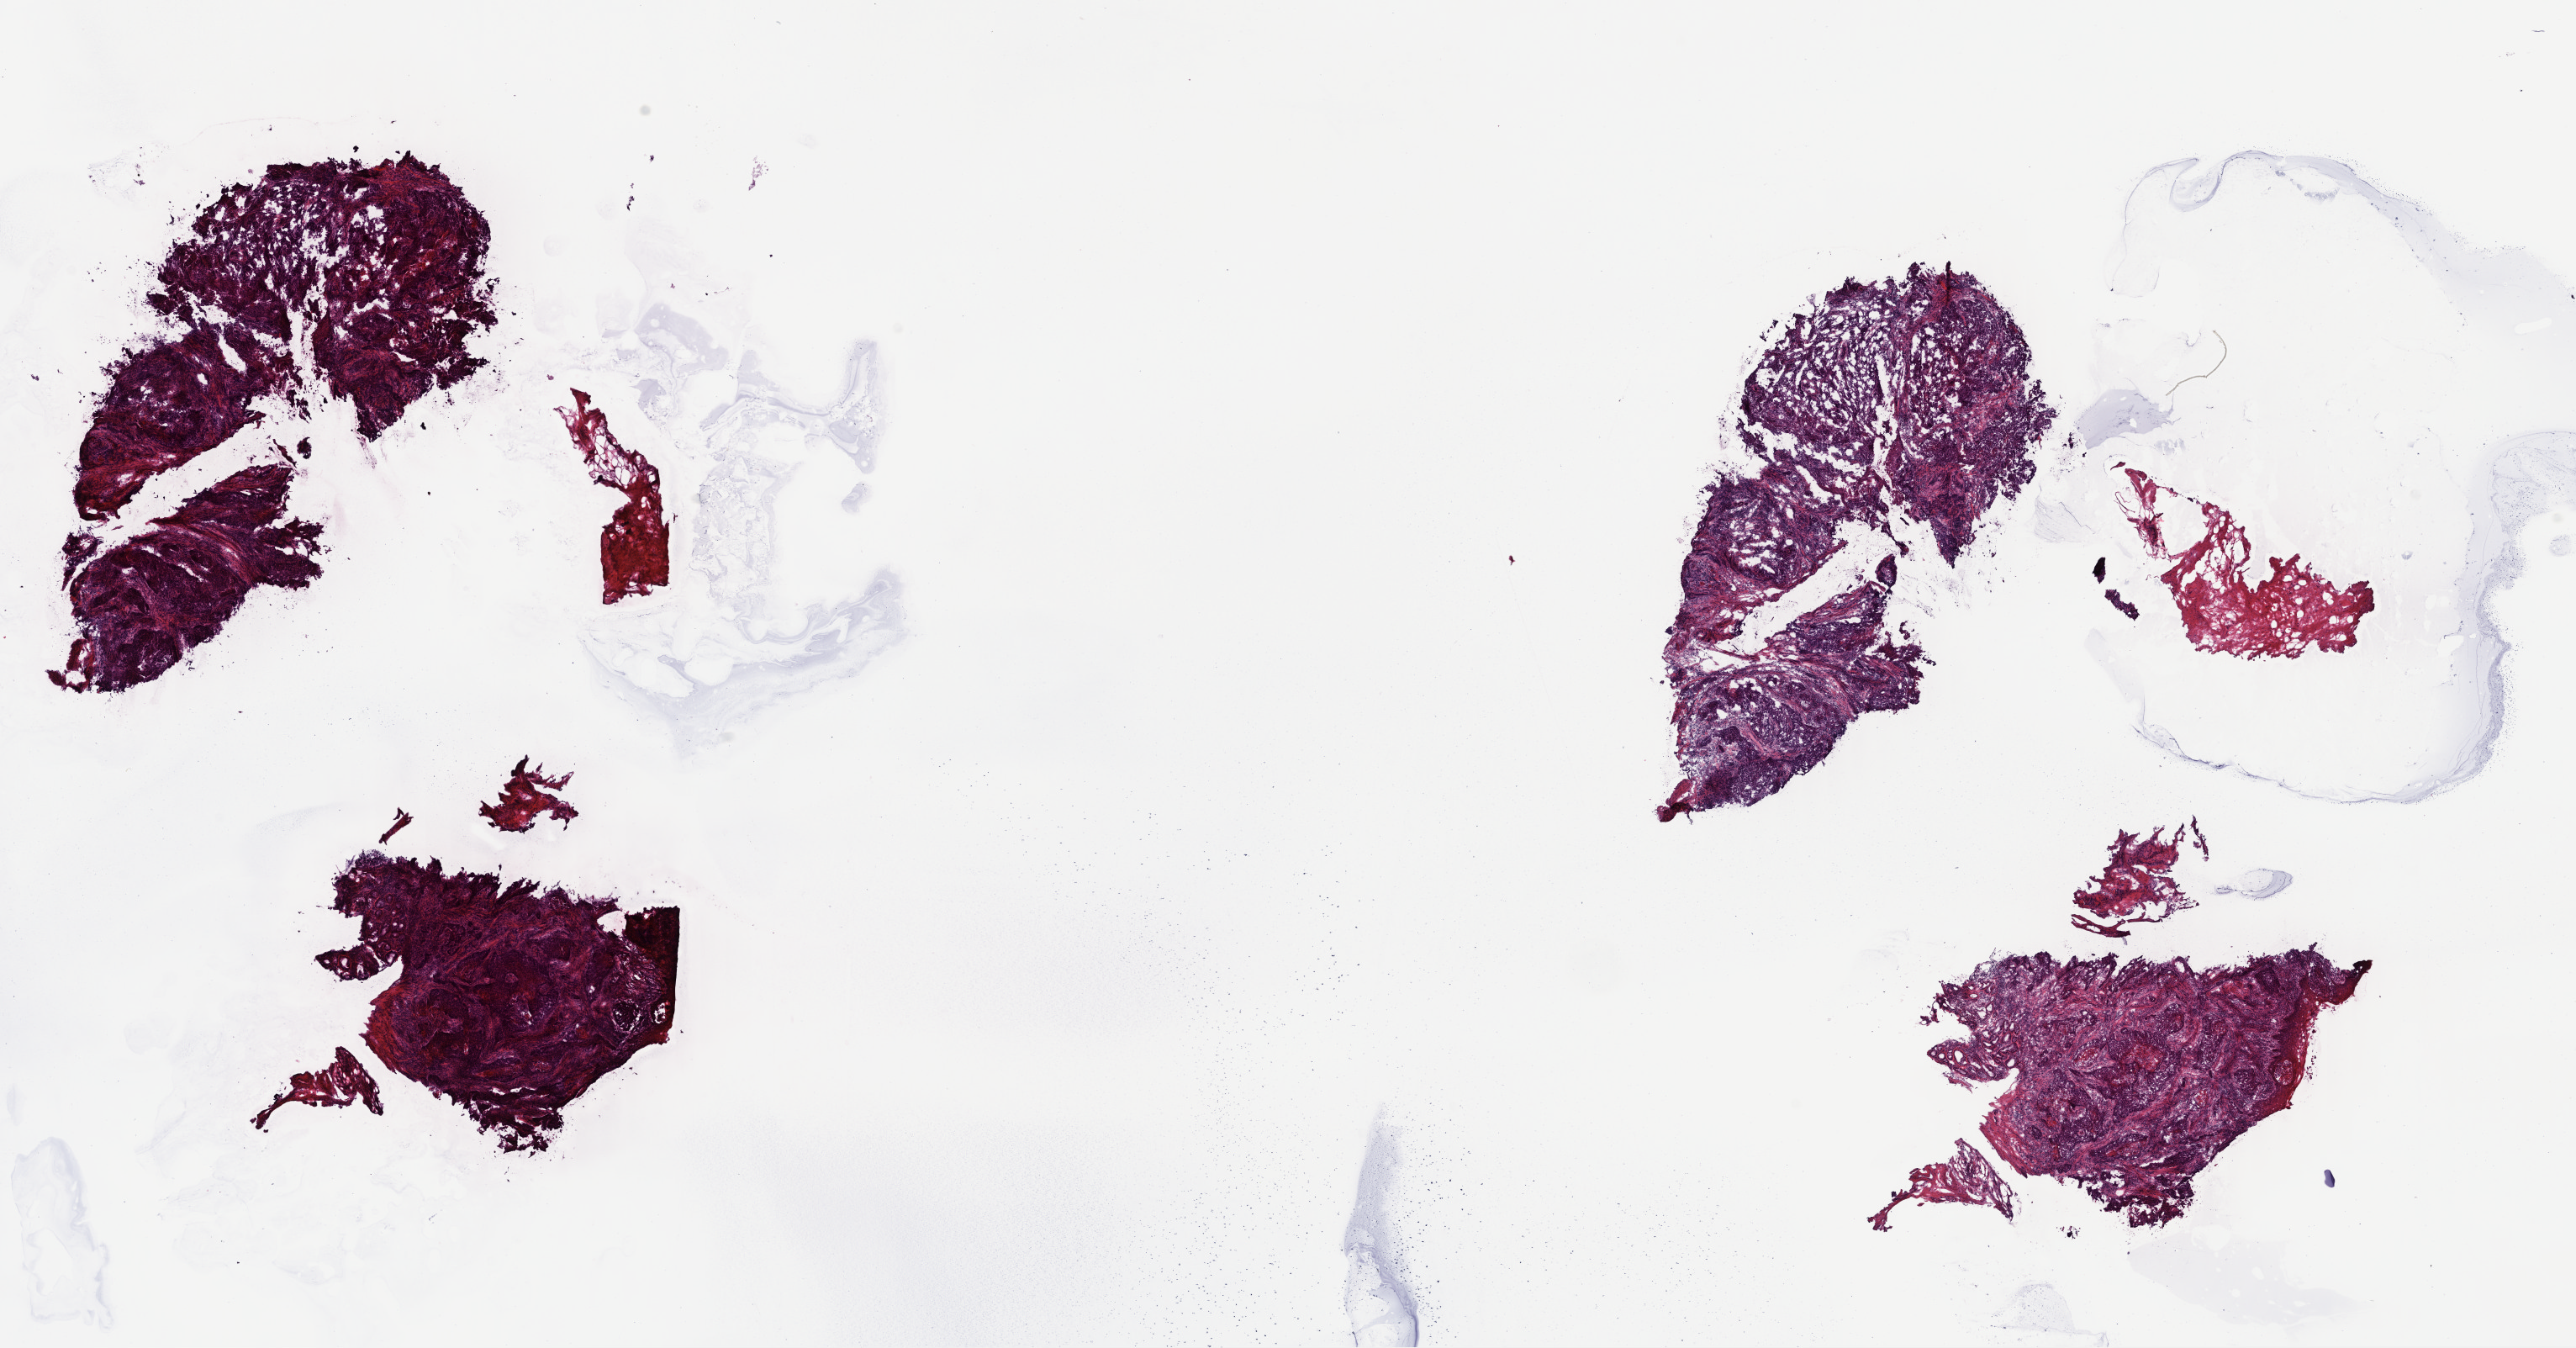
Whole-slide histology image, H&E, whole scanned area (about 24.1 x 12.6 mm, from a 40x scan) shown as a low-resolution overview, frozen section from the top of the tissue portion, sample: primary tumour, head and neck. Male patient; age at initial diagnosis 75 years. Histologic grade: G3 (poorly differentiated). Slide review estimates, as recorded: tumour cells 80%, tumour nuclei 70%, normal cells 0%, stromal cells 20%, necrosis 0%. Infiltration values recorded for this section: lymphocyte infiltration 100%, monocyte infiltration 0%, neutrophil infiltration 0%.
Pathologic diagnosis: Squamous cell carcinoma, NOS (larynx, NOS). Lymph nodes positive (case pathology): 0 of 10 examined.